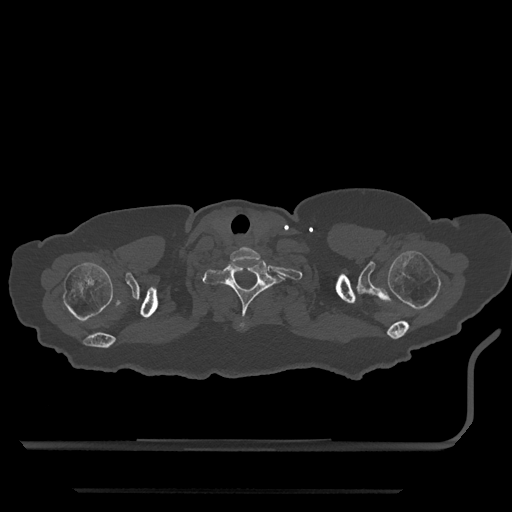
CT including the spine, one axial slice; position 714 of 797 along the scan axis; bone window (W 1800 / L 400 HU); 0.5 mm slice thickness; 512 × 512 image matrix. Female patient, age 51 years. Case-level facts recorded for this patient, not image findings: primary cancer: neuro; vertebrae with lytic lesions (as recorded): T8.
Annotated regions visible in this slice (semi-automatic segmentation, software-assisted and operator-edited):
- T1 vertebra: bounding box (x1, y1, x2, y2) in pixels: (203, 260, 285, 330)